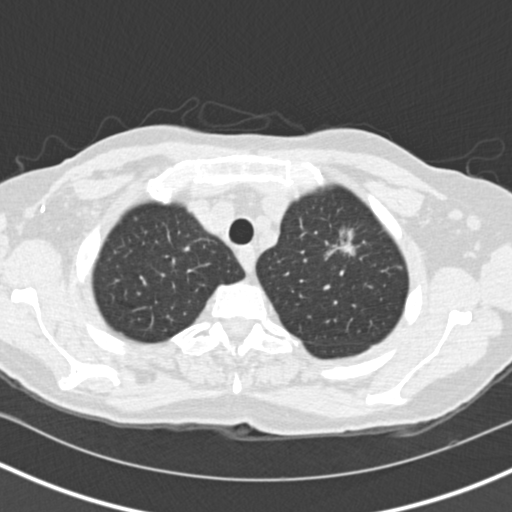
Low-dose screening chest CT, one axial slice. Lung window (W 1500 / L -600 HU). 2 mm slice thickness. 512 × 512 image matrix.
Annotated regions visible in this slice (manually delineated by an expert):
- lesion 1 (tumor, upper lobe of left lung): bounding box (x1, y1, x2, y2) in pixels: (334, 229, 355, 256)